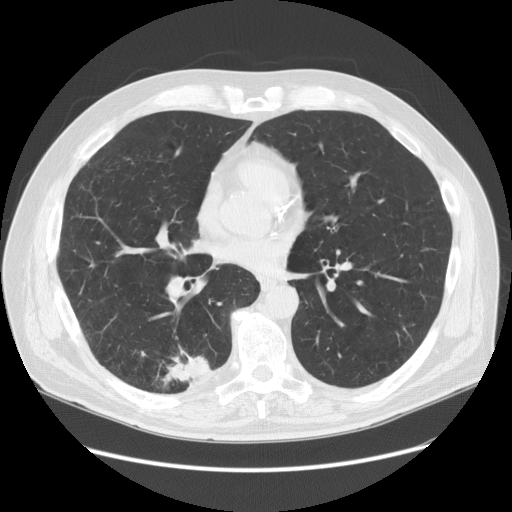
Low-dose screening chest CT, one axial slice. Slice 70 of 149 in the series (ordered by position). Reconstruction kernel STANDARD. 120 kVp. Lung window (W 1500 / L -600 HU). 512 × 512 image matrix.
Annotated regions visible in this slice (outlined manually by an expert reader):
- lesion 1 (tumor, lower lobe of right lung): box from (x=162, y=347) to (x=214, y=387) px